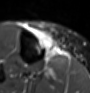
MRI of an extremity soft-tissue mass, one axial slice. Slice 22 of 60 in the series (ordered by position). STIR. MR volume resampled by the dataset authors to the PET/CT grid (not the native acquisition matrix). 3.27 mm slice thickness. 90 × 93 image matrix, field of view 88 × 91 mm. Female patient. Case-level facts recorded for this patient, not image findings: histological type: undifferentiated – high grade; grade: high; site of the primary tumour: right thigh.
Annotated regions visible in this slice (expert contour drawn on MRI and transferred to this co-registered scan by the dataset authors):
- gross tumour volume (mass): box from (x=37, y=30) to (x=59, y=59) px